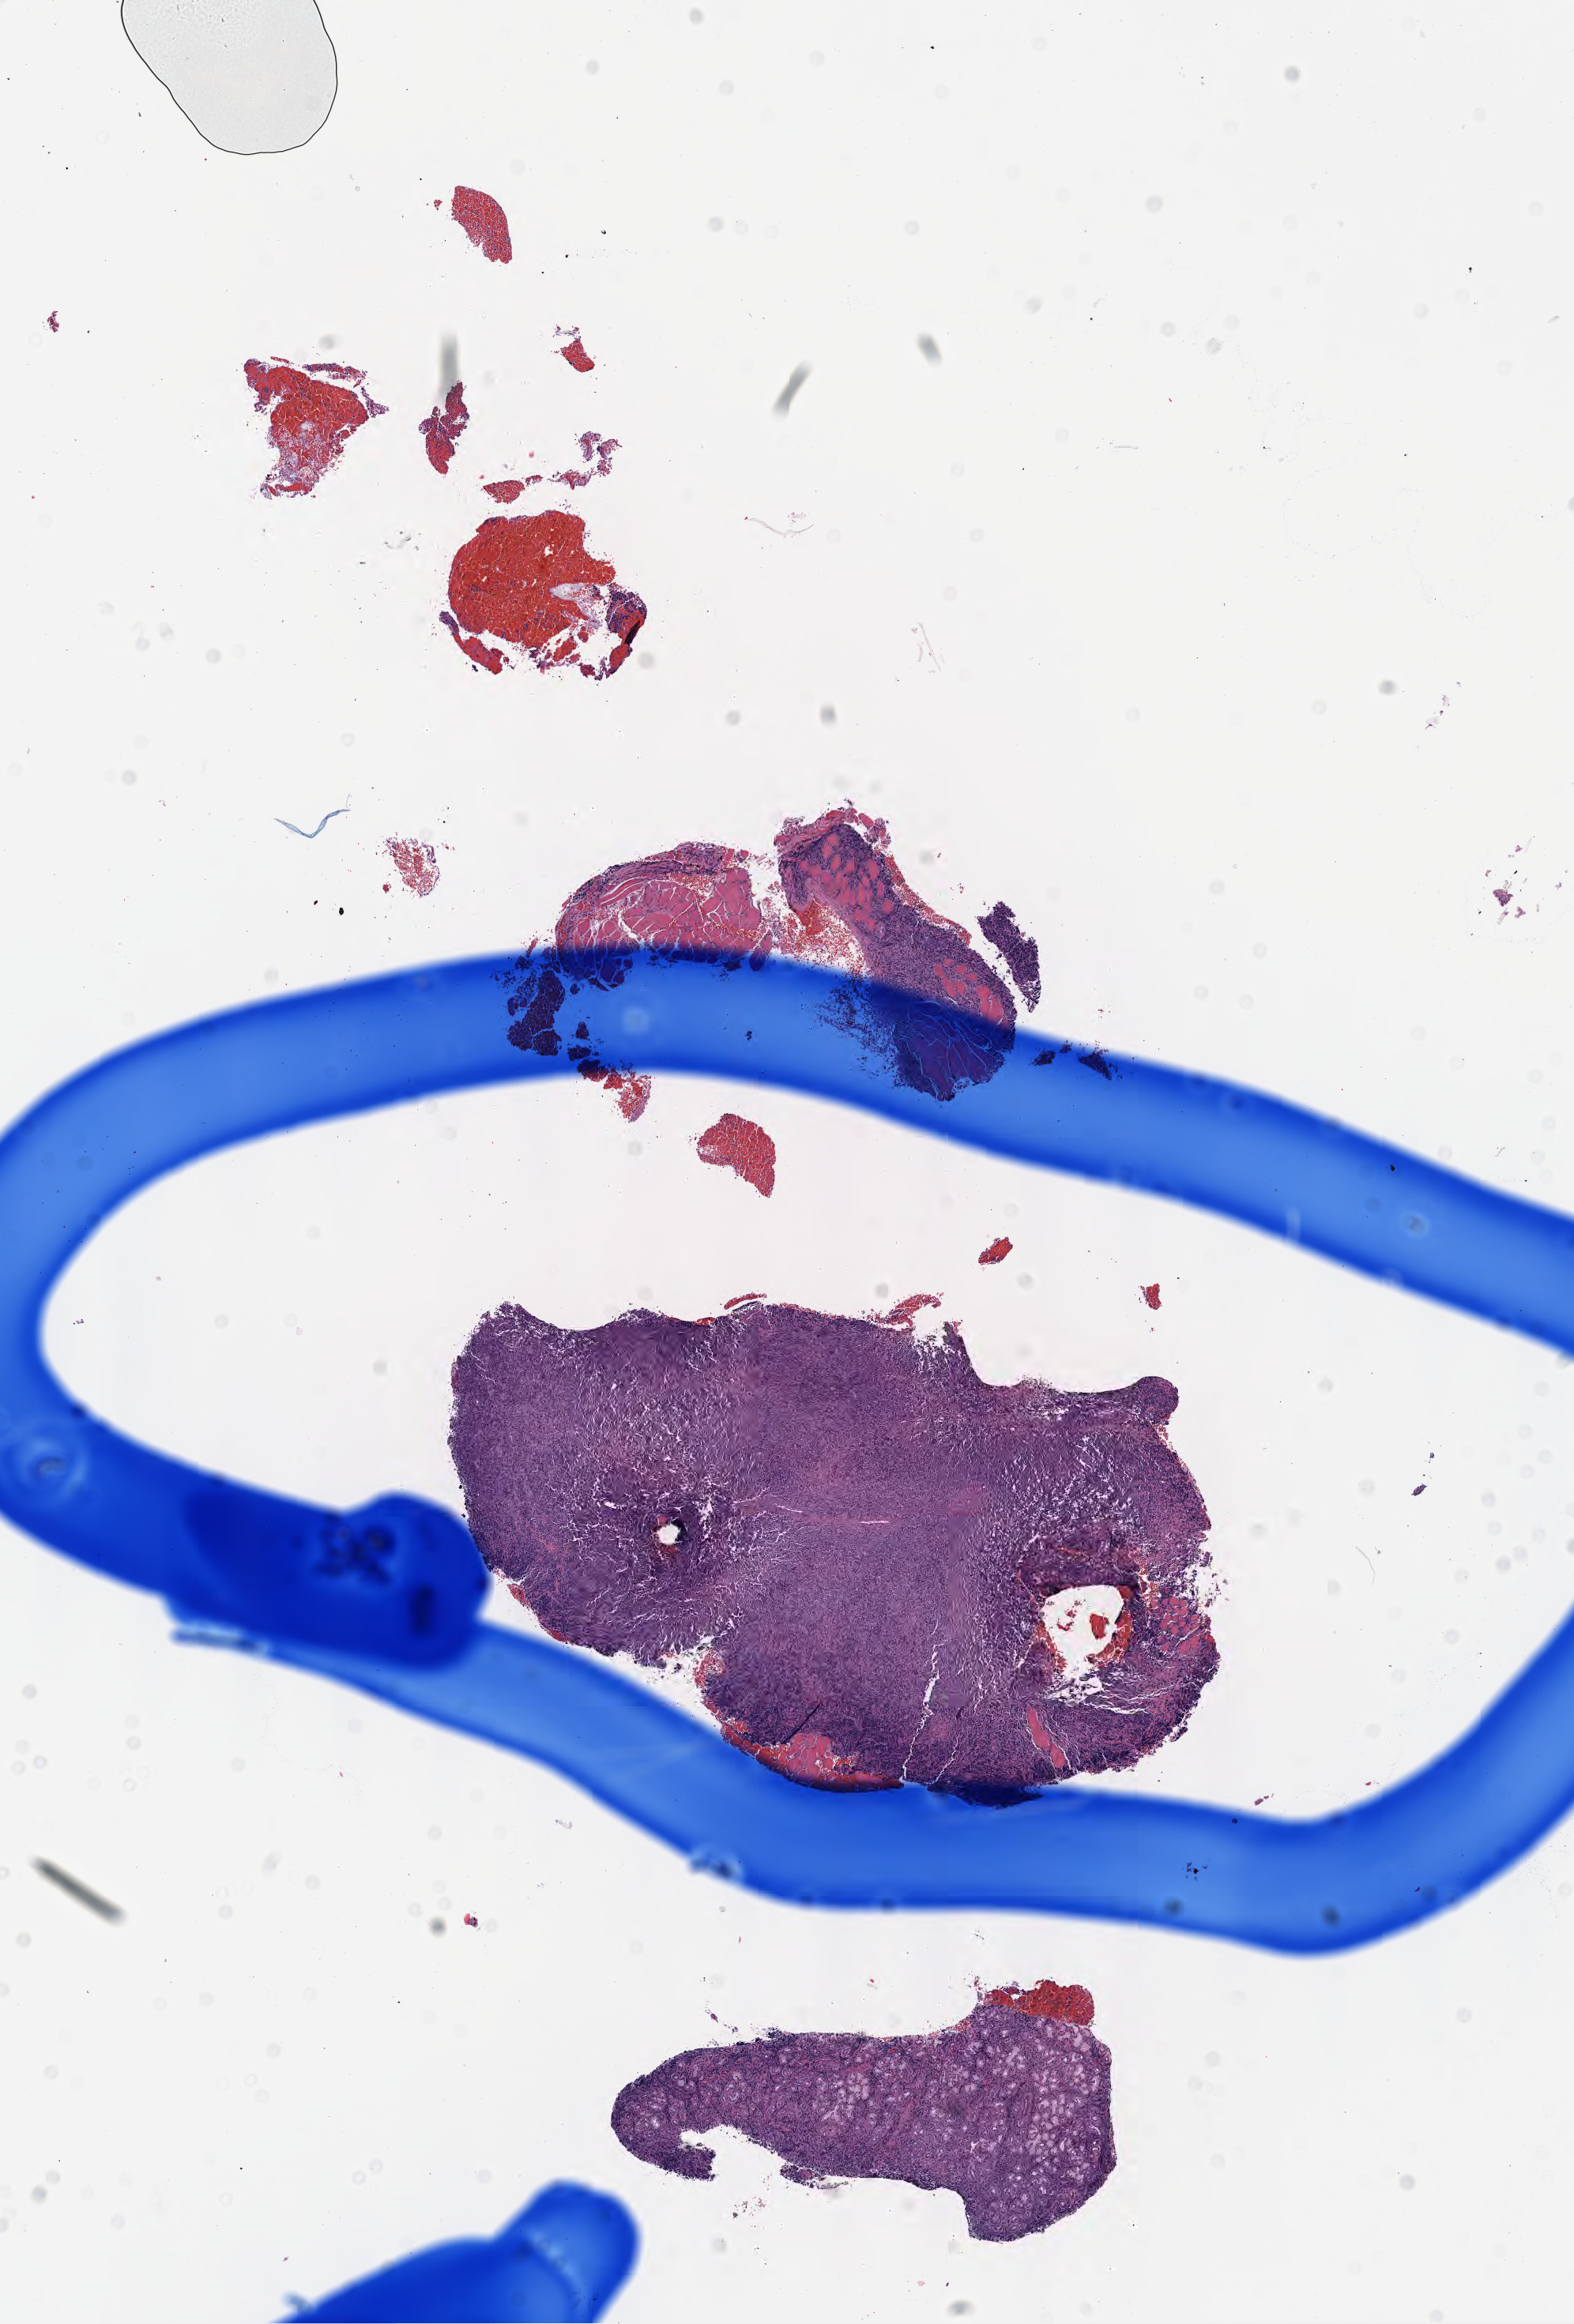
Digitized H&E-stained section, low-resolution overview of the scanned area, about 8.0 x 11.9 mm, tumor tissue. Patient male; 53 years old.
* diagnosis: Diffuse large B-cell lymphoma, NOS